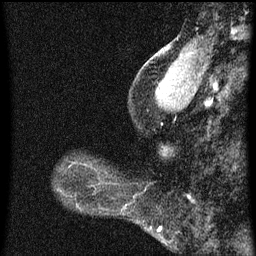
Breast MRI (dynamic contrast-enhanced), one sagittal slice; slice 17 of 60 in the series (ordered by position); dynamic contrast-enhanced series, image 2 of 3 at this slice position (ordered by acquisition); 1.5 T; TE 4.2 ms, TR 8 ms; 256 × 256 image matrix, field of view 180 × 180 mm. Female patient, age 44 years.
Outlined on this slice (semi-automatically segmented with operator editing):
- analysis volume of interest (the breast-tissue region the enhancement analysis was run in; not a lesion): box from (x=62, y=158) to (x=95, y=169) px
- tumour enhancement mask (voxels above the 70 % enhancement threshold inside the analysis volume of interest): (x=68, y=164)–(x=75, y=169)